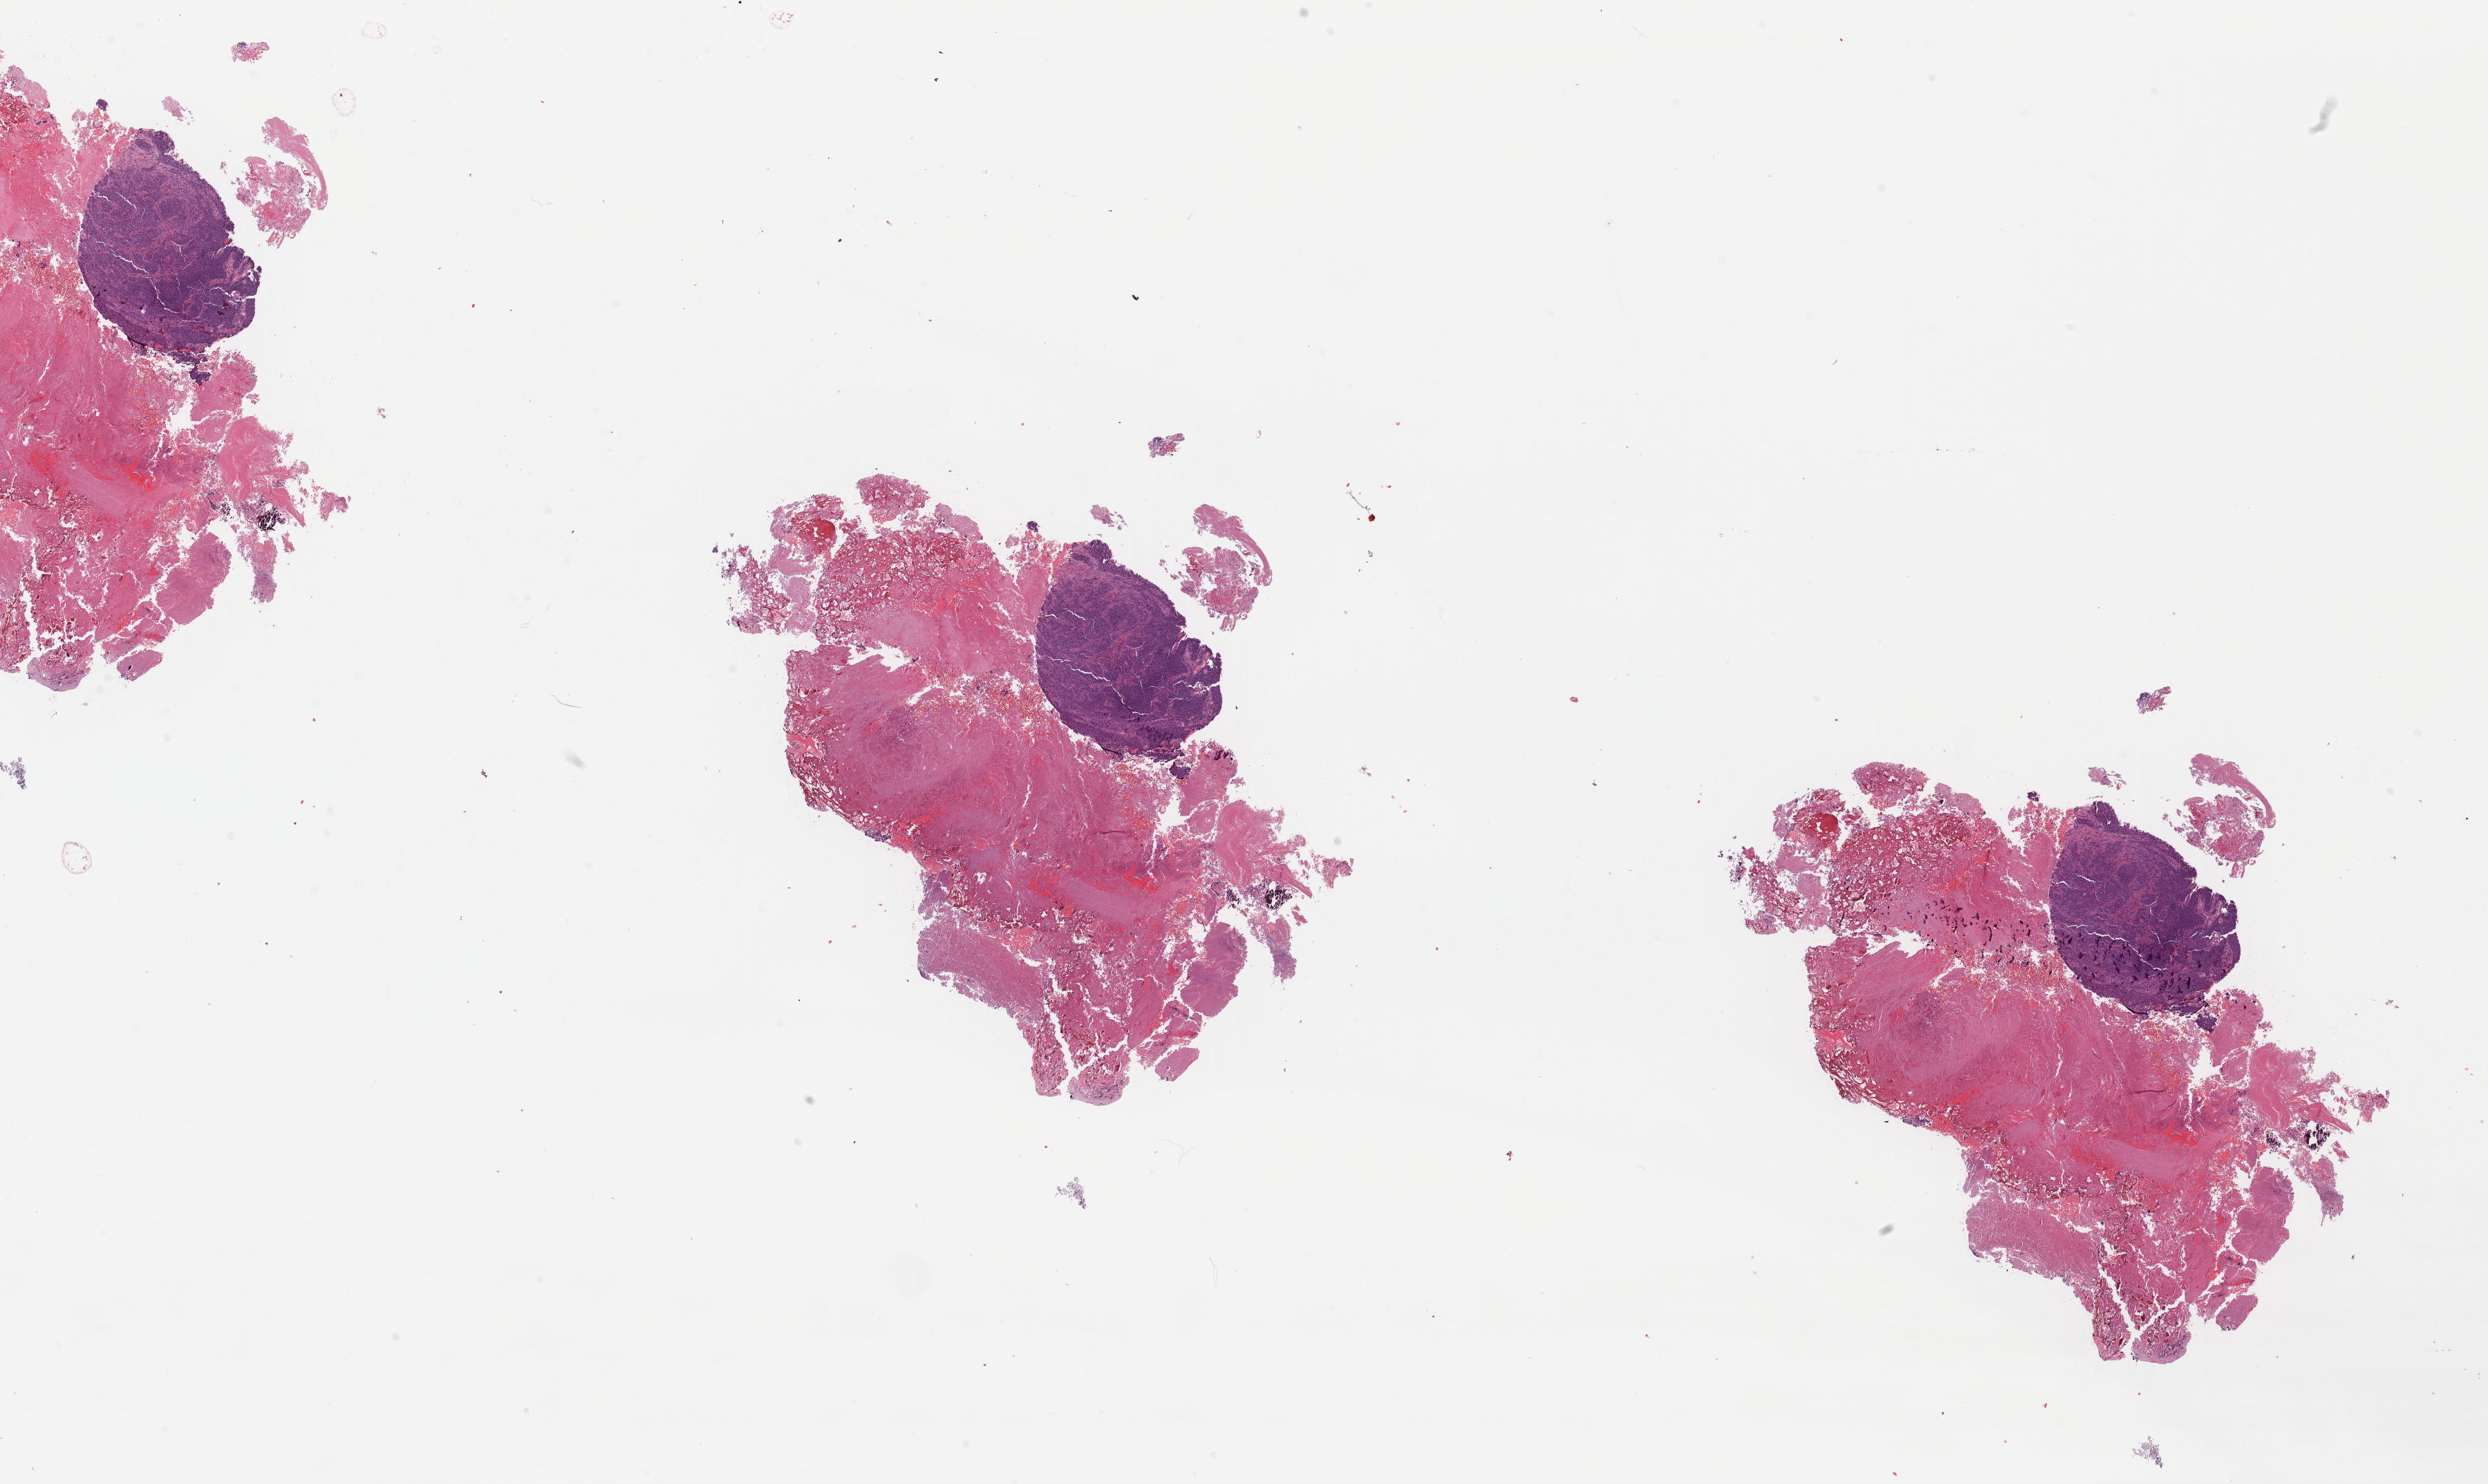
H&E whole-slide image, shown as a low-resolution overview of the whole scanned area (about 28.3 x 16.9 mm, acquisition: 40x scan); FFPE section; sample: primary tumour, bladder. Patient: male, age at initial diagnosis 64 years. Histologic grade: high grade.
* AJCC pathologic stage: III (7th edition)
* lymph nodes positive (case pathology): 0 of 28 examined
* histologic diagnosis: Transitional cell carcinoma